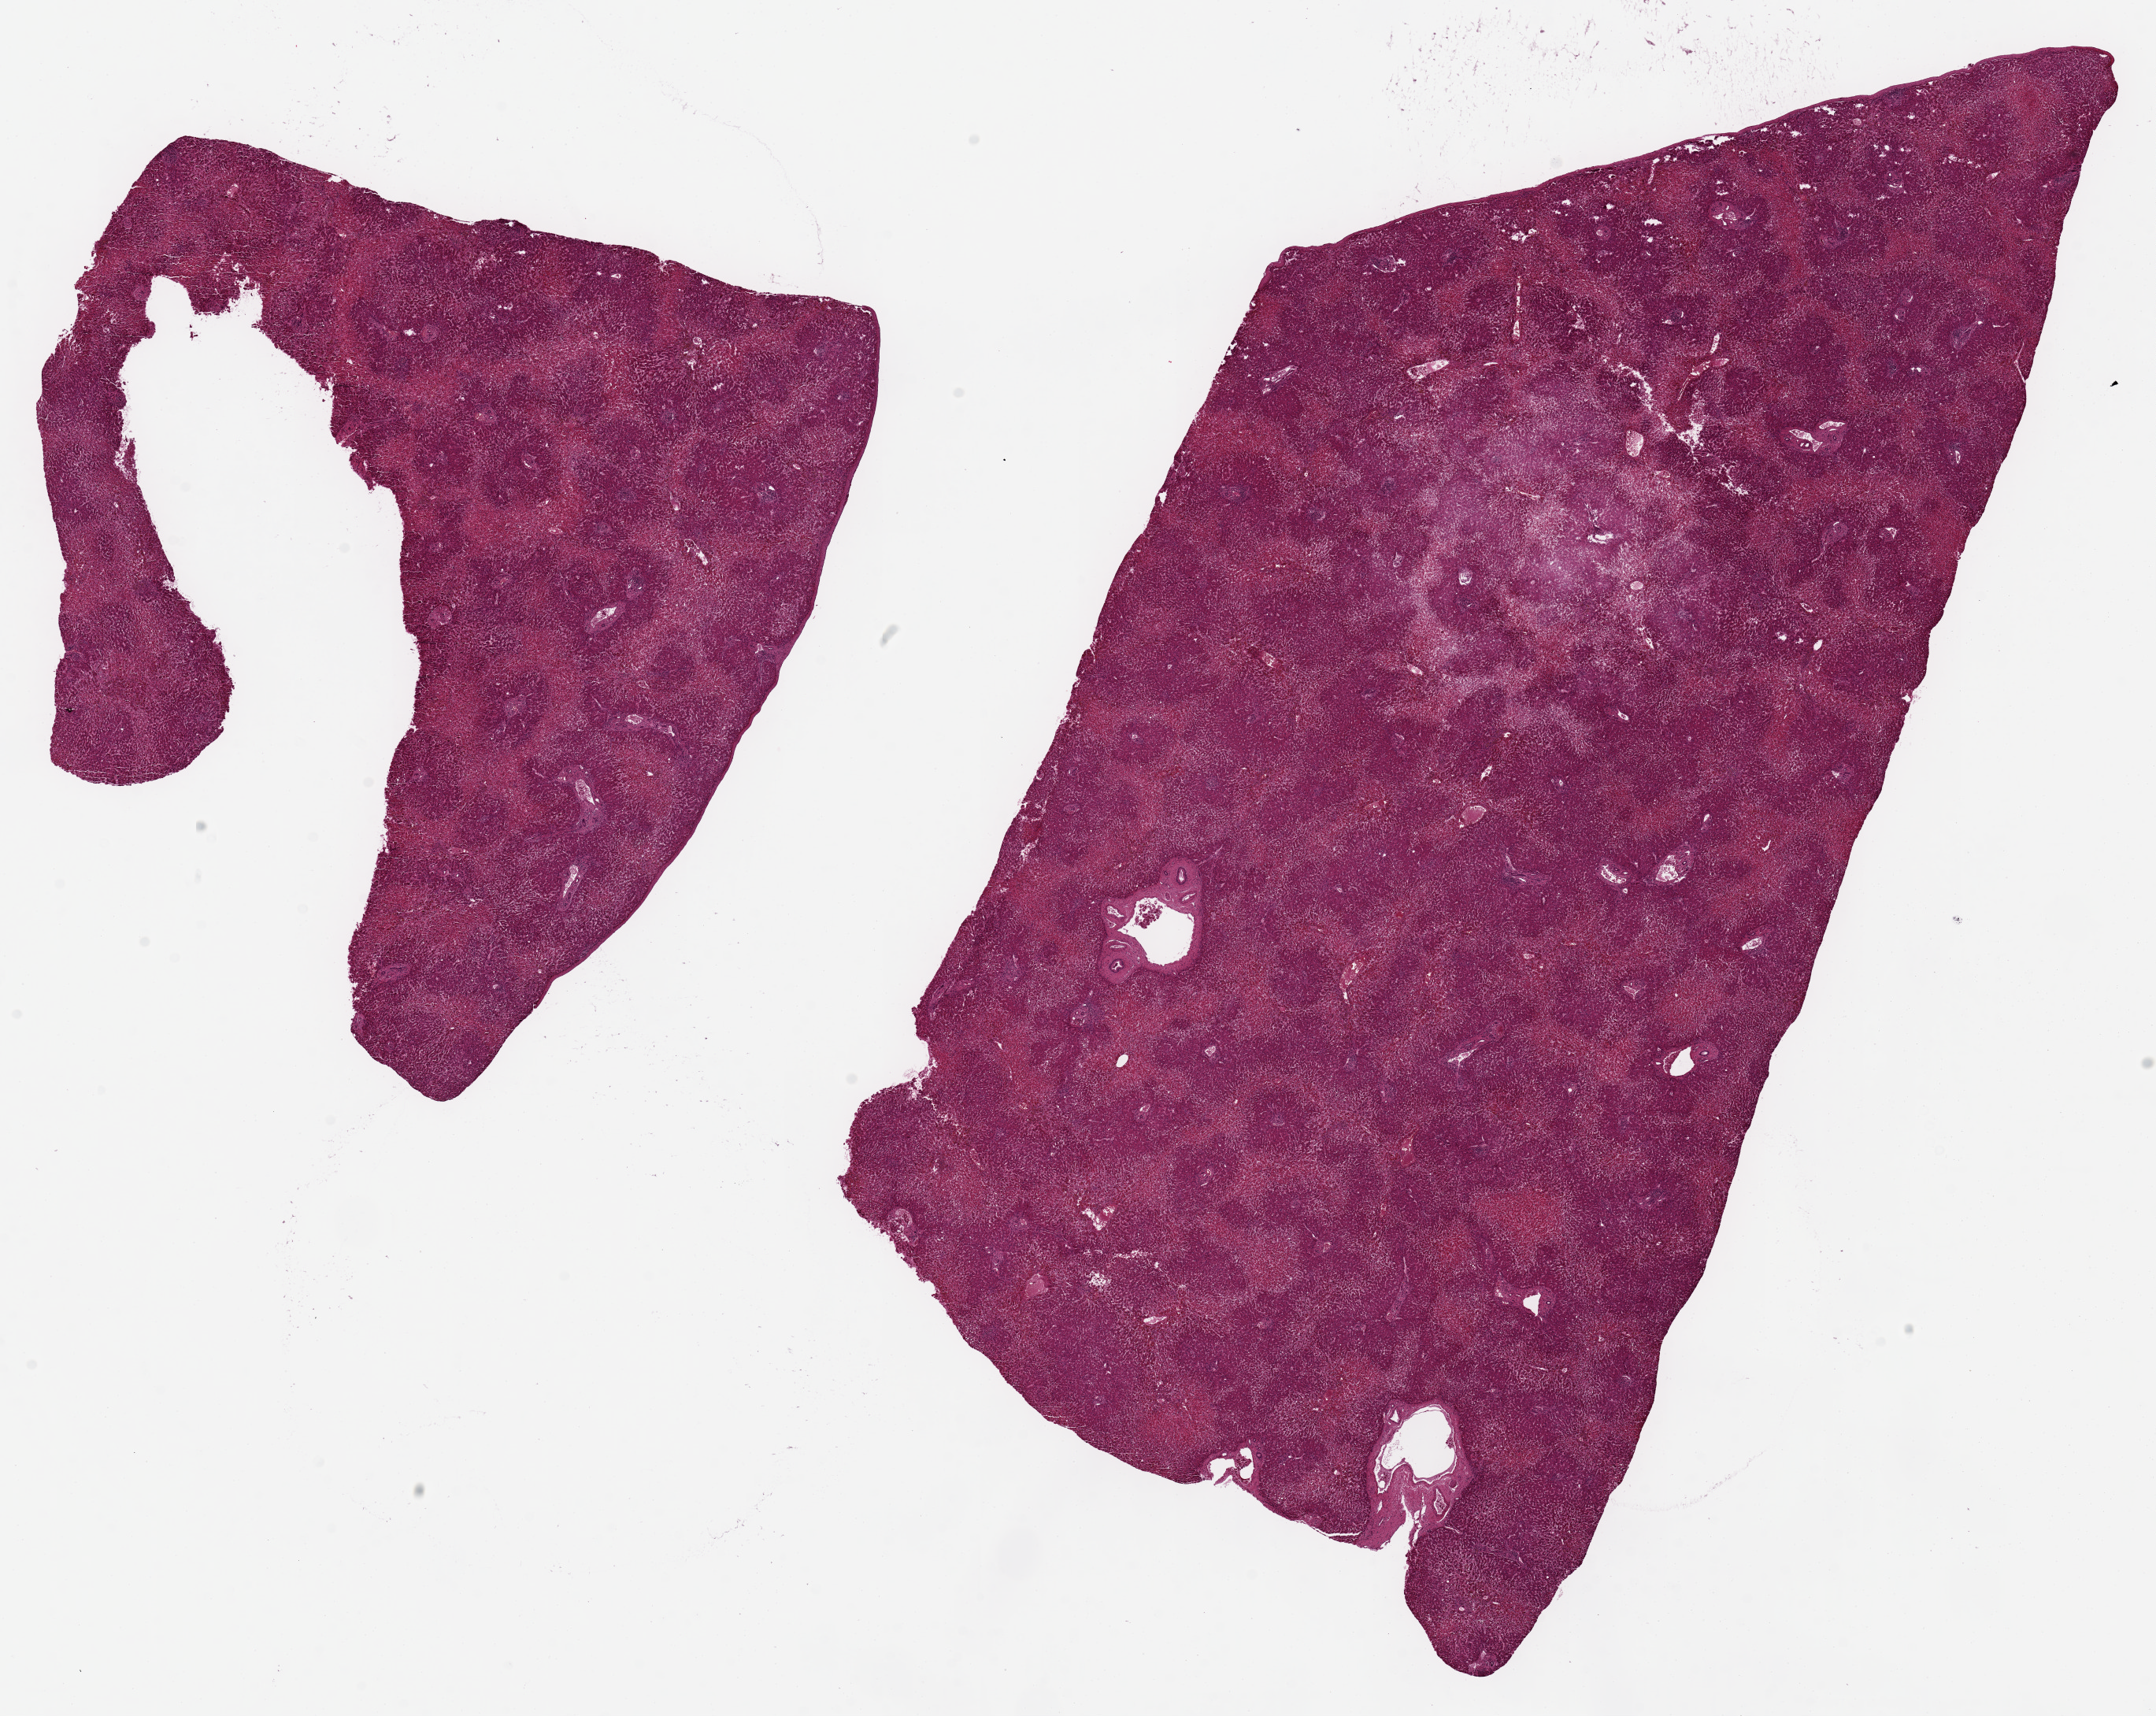
Digitized H&E-stained section — shown as a low-resolution overview of the whole scanned area (about 21.7 x 17.2 mm). PAXgene-fixed, paraffin-embedded tissue. Target tissue: liver. Donor tissue sample. Female donor.
Reviewer comment on this tissue sample: 2 pieces, 9x8 & 17.5x8mm; Marked midzonal necrosis.